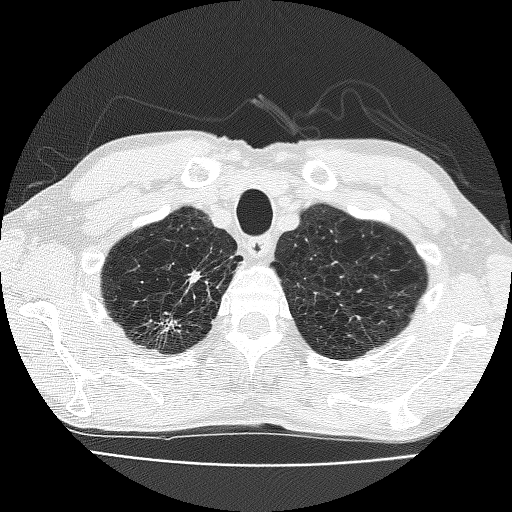
Low-dose screening chest CT, one axial slice; position 154 of 185 along the scan axis; reconstruction kernel FC51; lung window (W 1500 / L -600 HU); 2 mm slice thickness; 512 × 512 image matrix, field of view 322 × 322 mm.
Outlined on this slice (manually delineated by an expert):
- lesion 1 (nodule, upper lobe of right lung): box from (x=189, y=271) to (x=200, y=283) px
- lesion 2 (nodule, upper lobe of right lung): (x=160, y=318)–(x=180, y=332)